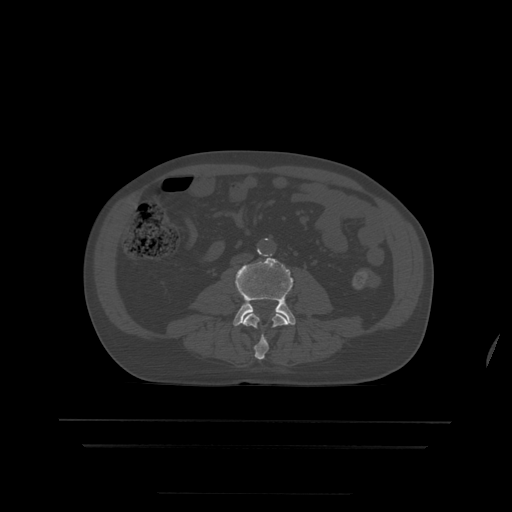
CT including the spine, one axial slice. Position 106 of 522 along the scan axis. Bone window (W 1800 / L 400 HU). 512 × 512 image matrix, field of view 436 × 436 mm. Patient age 68 years. From the clinical record (not read from this slice): primary cancer: urothelial.
Annotated regions visible in this slice (semi-automatic segmentation, software-assisted and operator-edited):
- L3 vertebra: bounding box [x1, y1, x2, y2] px = [242, 313, 290, 360]
- L4 vertebra: [233, 258, 296, 327]